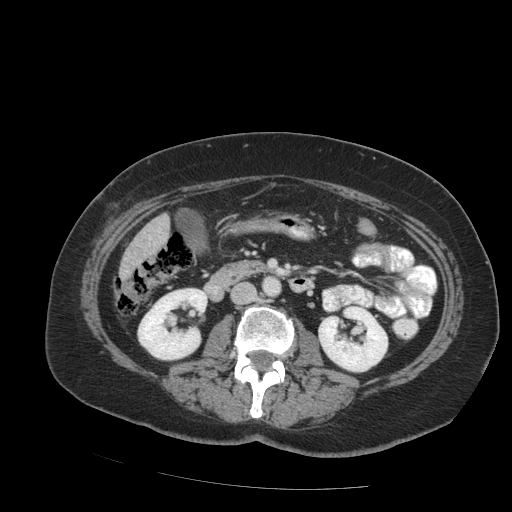
Contrast-enhanced abdominal CT (liver protocol), one axial slice; slice 24 of 99 in the series (ordered by position); reconstruction kernel STANDARD; 140 kVp; soft-tissue window (W 400 / L 40 HU); 2.5 mm slice thickness; 512 × 512 image matrix, field of view 400 × 400 mm. From the clinical record (not read from this slice): diagnosis: hepatocellular carcinoma (patient treated with transarterial chemoembolisation; whether this scan precedes or follows treatment is not stated here); TNM stage (as recorded): Stage-IVB; Child-Pugh class: A; tumour differentiation: moderately differentiated; tumour nodularity: uninodular.
Structures marked on this image (semi-automatic segmentation, software-assisted and operator-edited):
- liver parenchyma outside the tumour (the mass and vessels are separate outlines, so this box may not span the whole liver): box from (x=118, y=214) to (x=170, y=280) px